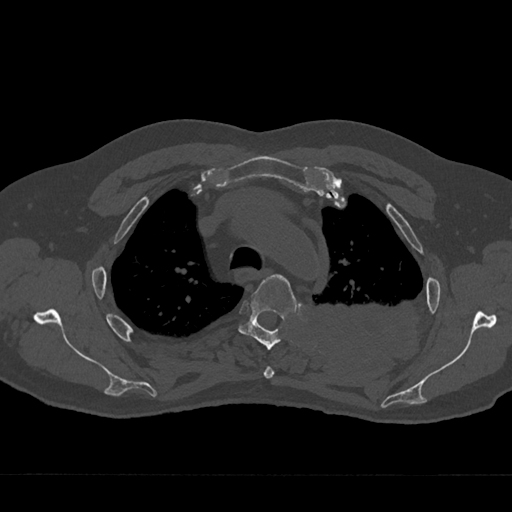
CT including the spine, one axial slice. Position 528 of 797 along the scan axis. Reconstruction kernel Br40s/3. 120 kVp. Bone window (W 1800 / L 400 HU). 0.5 mm slice thickness. 512 × 512 image matrix. Patient: male, 75 years. From the clinical record (not read from this slice): primary cancer: renal; vertebrae with lytic lesions (as recorded): T4.
Outlined on this slice (semi-automatically segmented with operator editing):
- T3 vertebra: box from (x=263, y=367) to (x=275, y=379) px
- T4 vertebra: (x=238, y=274)–(x=297, y=350)